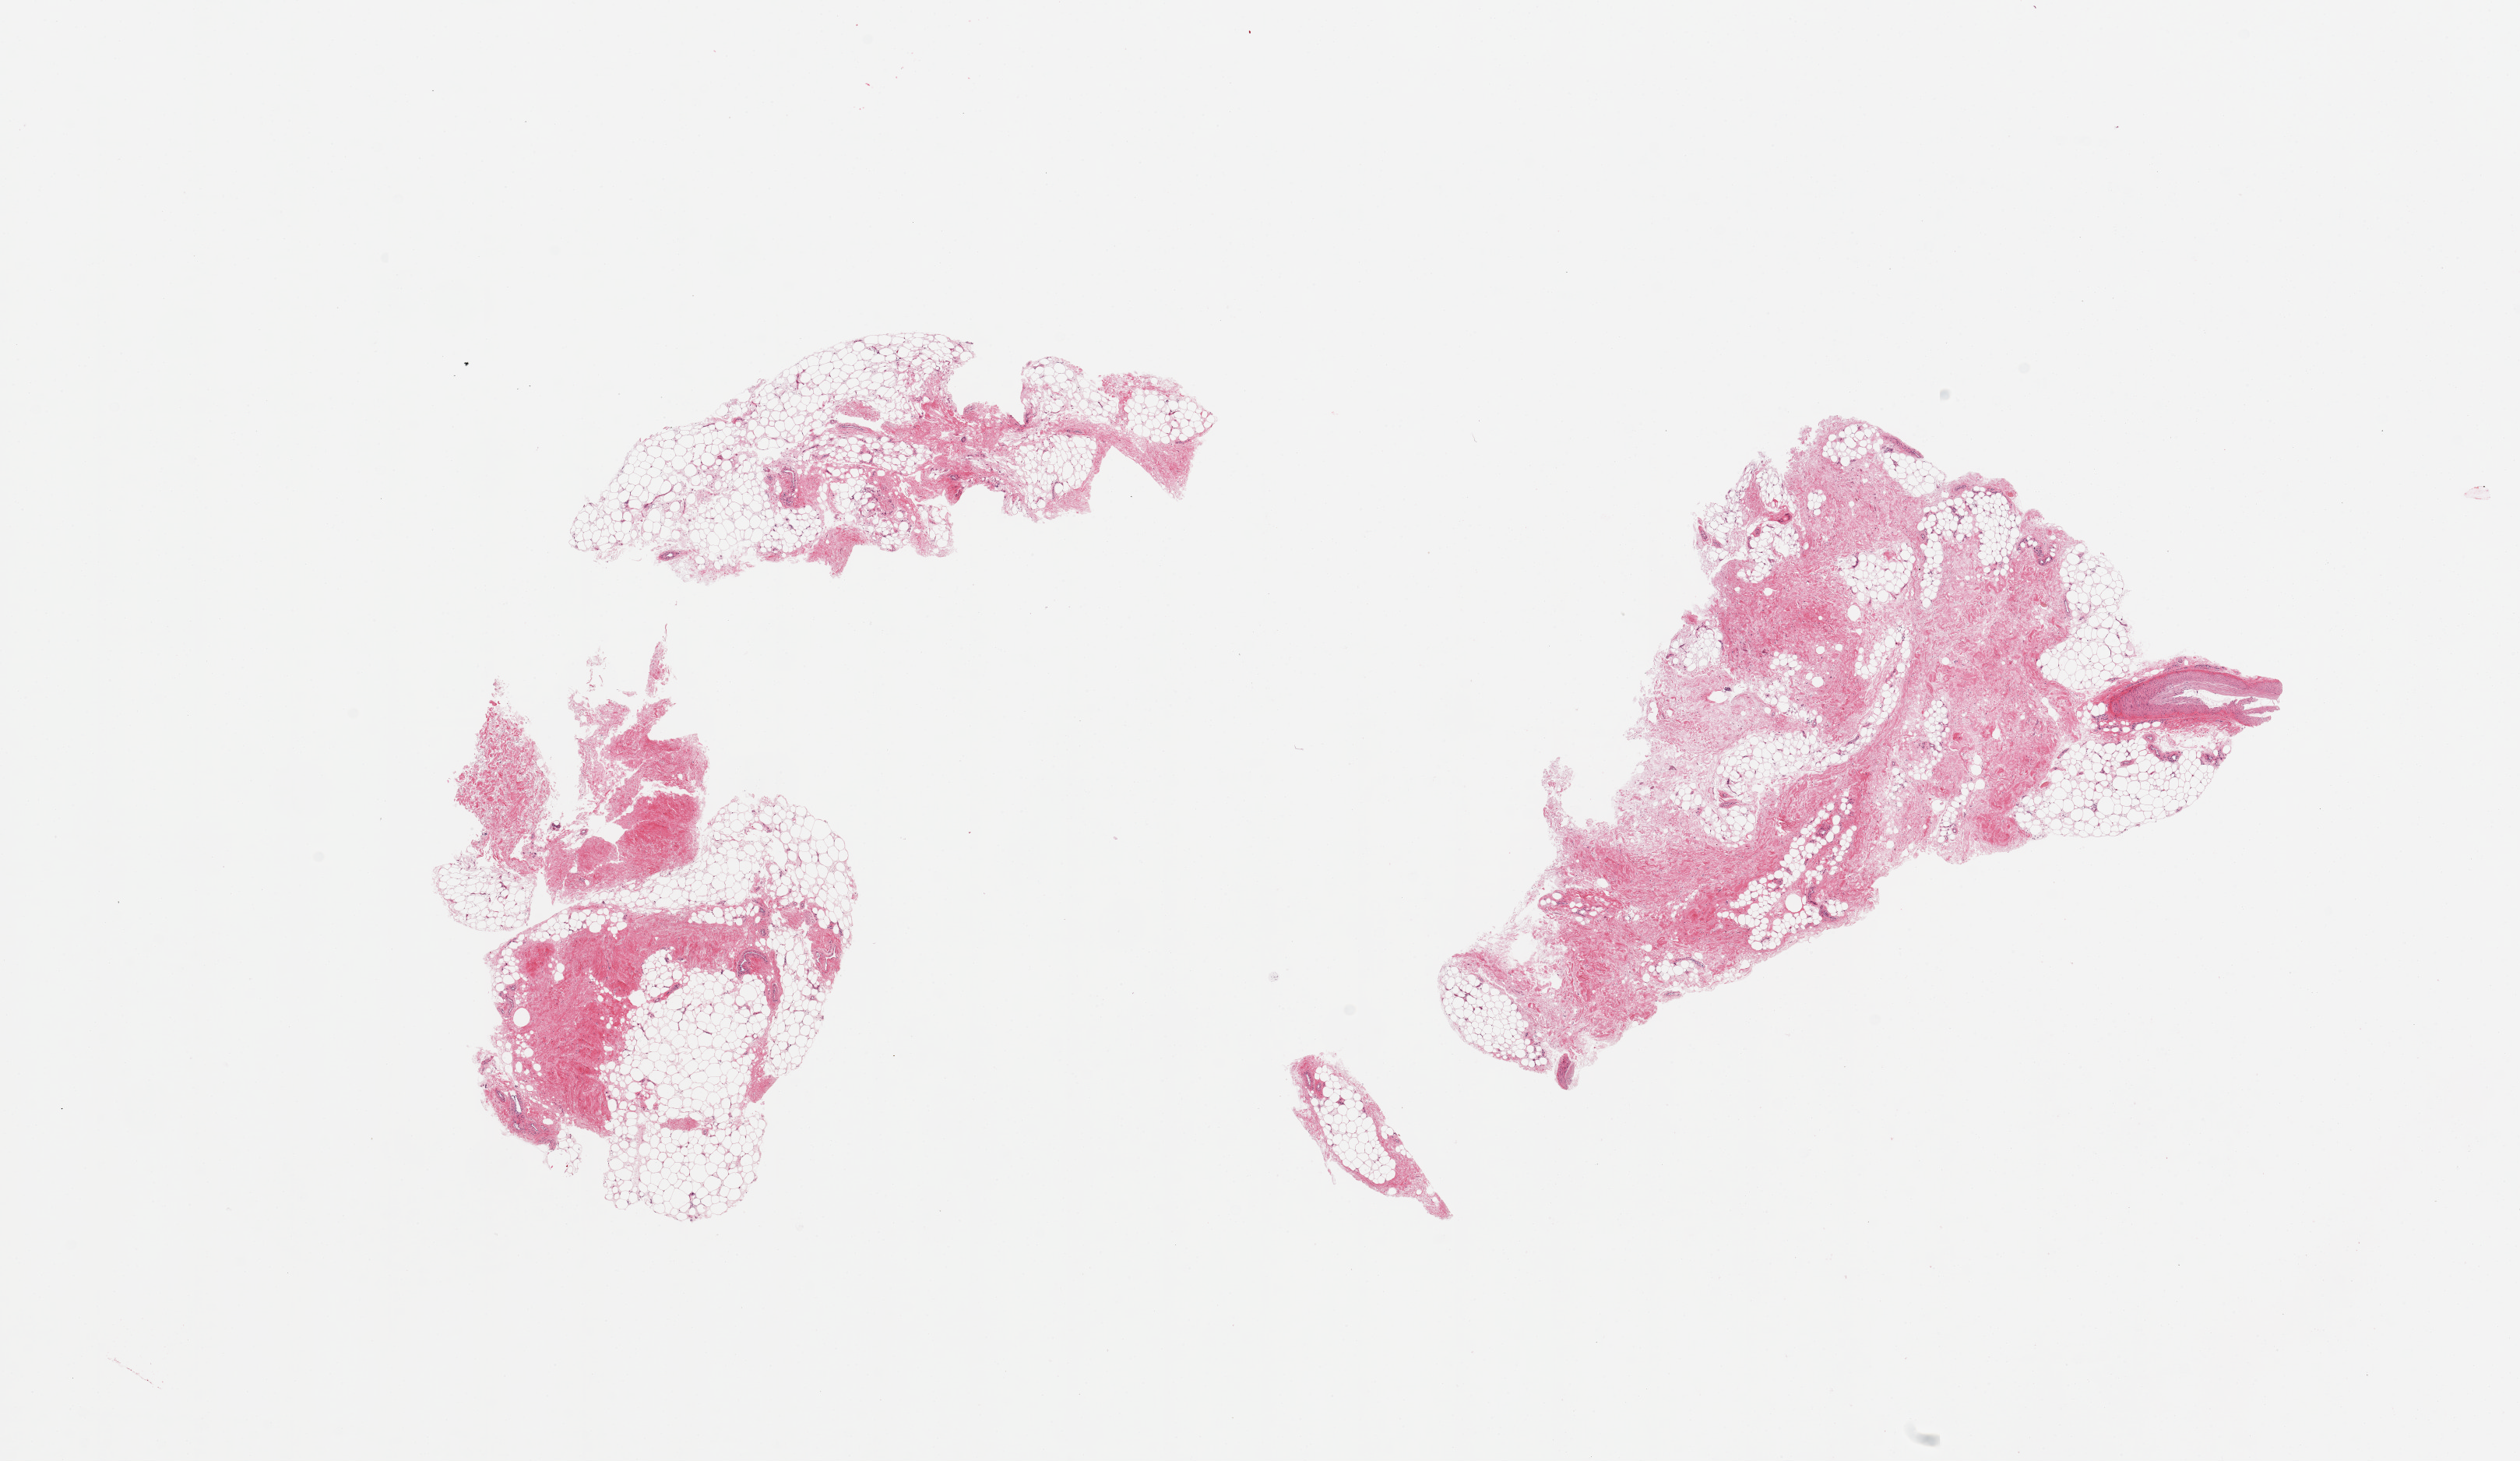
Digitized haematoxylin and eosin-stained section, shown as a low-resolution overview of the whole scanned area (about 25.6 x 14.8 mm); PAXgene-fixed paraffin-embedded (PFPE) section; target tissue: adipose tissue; tissue donor sample. Donor: male.
- pathologist's review note for this sample: 3 pieces; 10% to 50% fibrovascular component